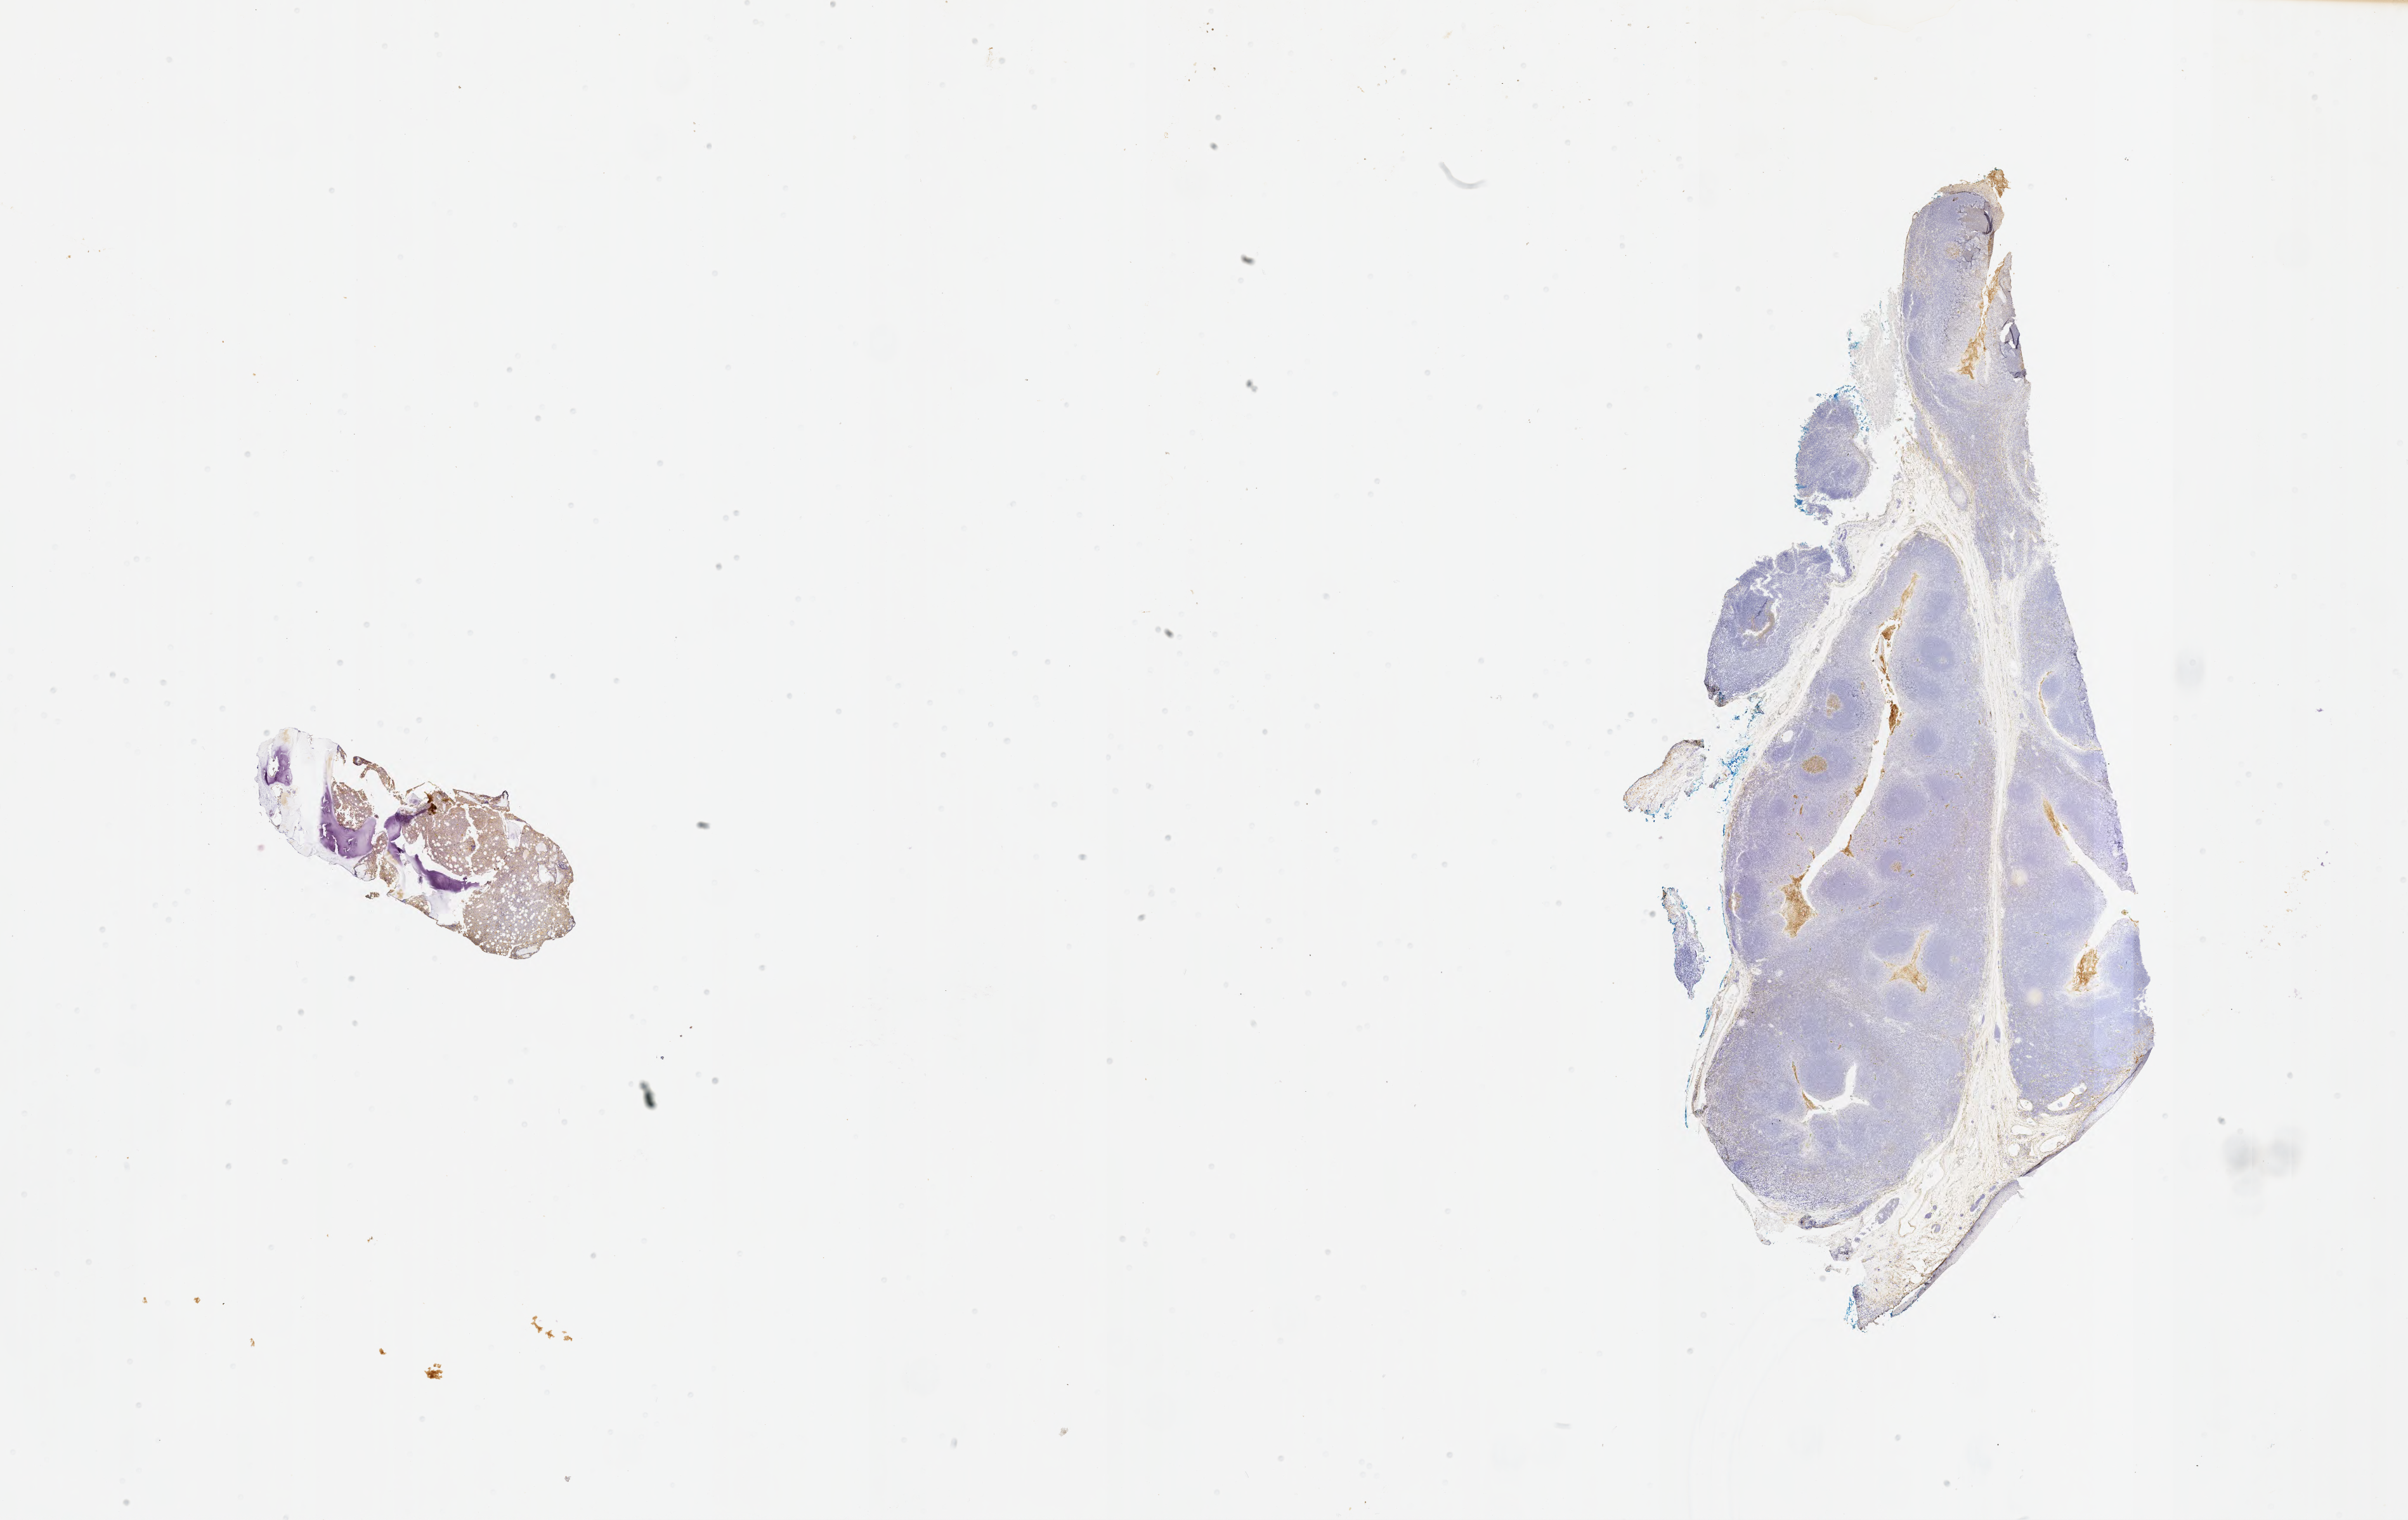
Immunohistochemistry (IHC) whole-slide image stained for CD10 — whole scanned area (about 30.7 x 19.4 mm) shown as a low-resolution overview. Tumor tissue. Site: bone marrow. Male patient, 15 years old.
• histologic diagnosis: Burkitt lymphoma, NOS